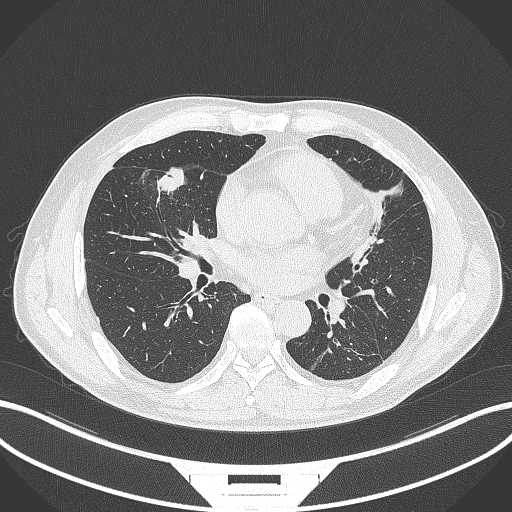
Chest CT, one axial slice; slice 148 of 399 in the series (ordered by position); reconstruction kernel B70f; 120 kVp; lung window (W 1500 / L -600 HU); 512 × 512 image matrix, field of view 400 × 400 mm. Male patient, age 59 years. Case-level facts recorded for this patient, not image findings: clinical TNM (as recorded): T2a N1 M0.
Outlined on this slice (rectangle marked by the reading radiologist):
- lung tumour (recorded histology: adenocarcinoma): box from (x=156, y=164) to (x=190, y=198) px